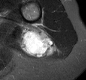
MRI of an extremity soft-tissue mass, one axial slice. Position 11 of 30 along the scan axis. STIR. MR volume resampled by the dataset authors to the PET/CT grid (not the native acquisition matrix). 3.27 mm slice thickness. 86 × 80 image matrix, field of view 84 × 78 mm. Female patient. Case-level facts recorded for this patient, not image findings: histological type: malignant fibrous histiocytoma; grade: low; site of the primary tumour: left arm.
Structures marked on this image (expert contour drawn on MRI and transferred to this co-registered scan by the dataset authors):
- gross tumour volume (mass): bounding box <19,24,55,59> (left, top, right, bottom; pixels)